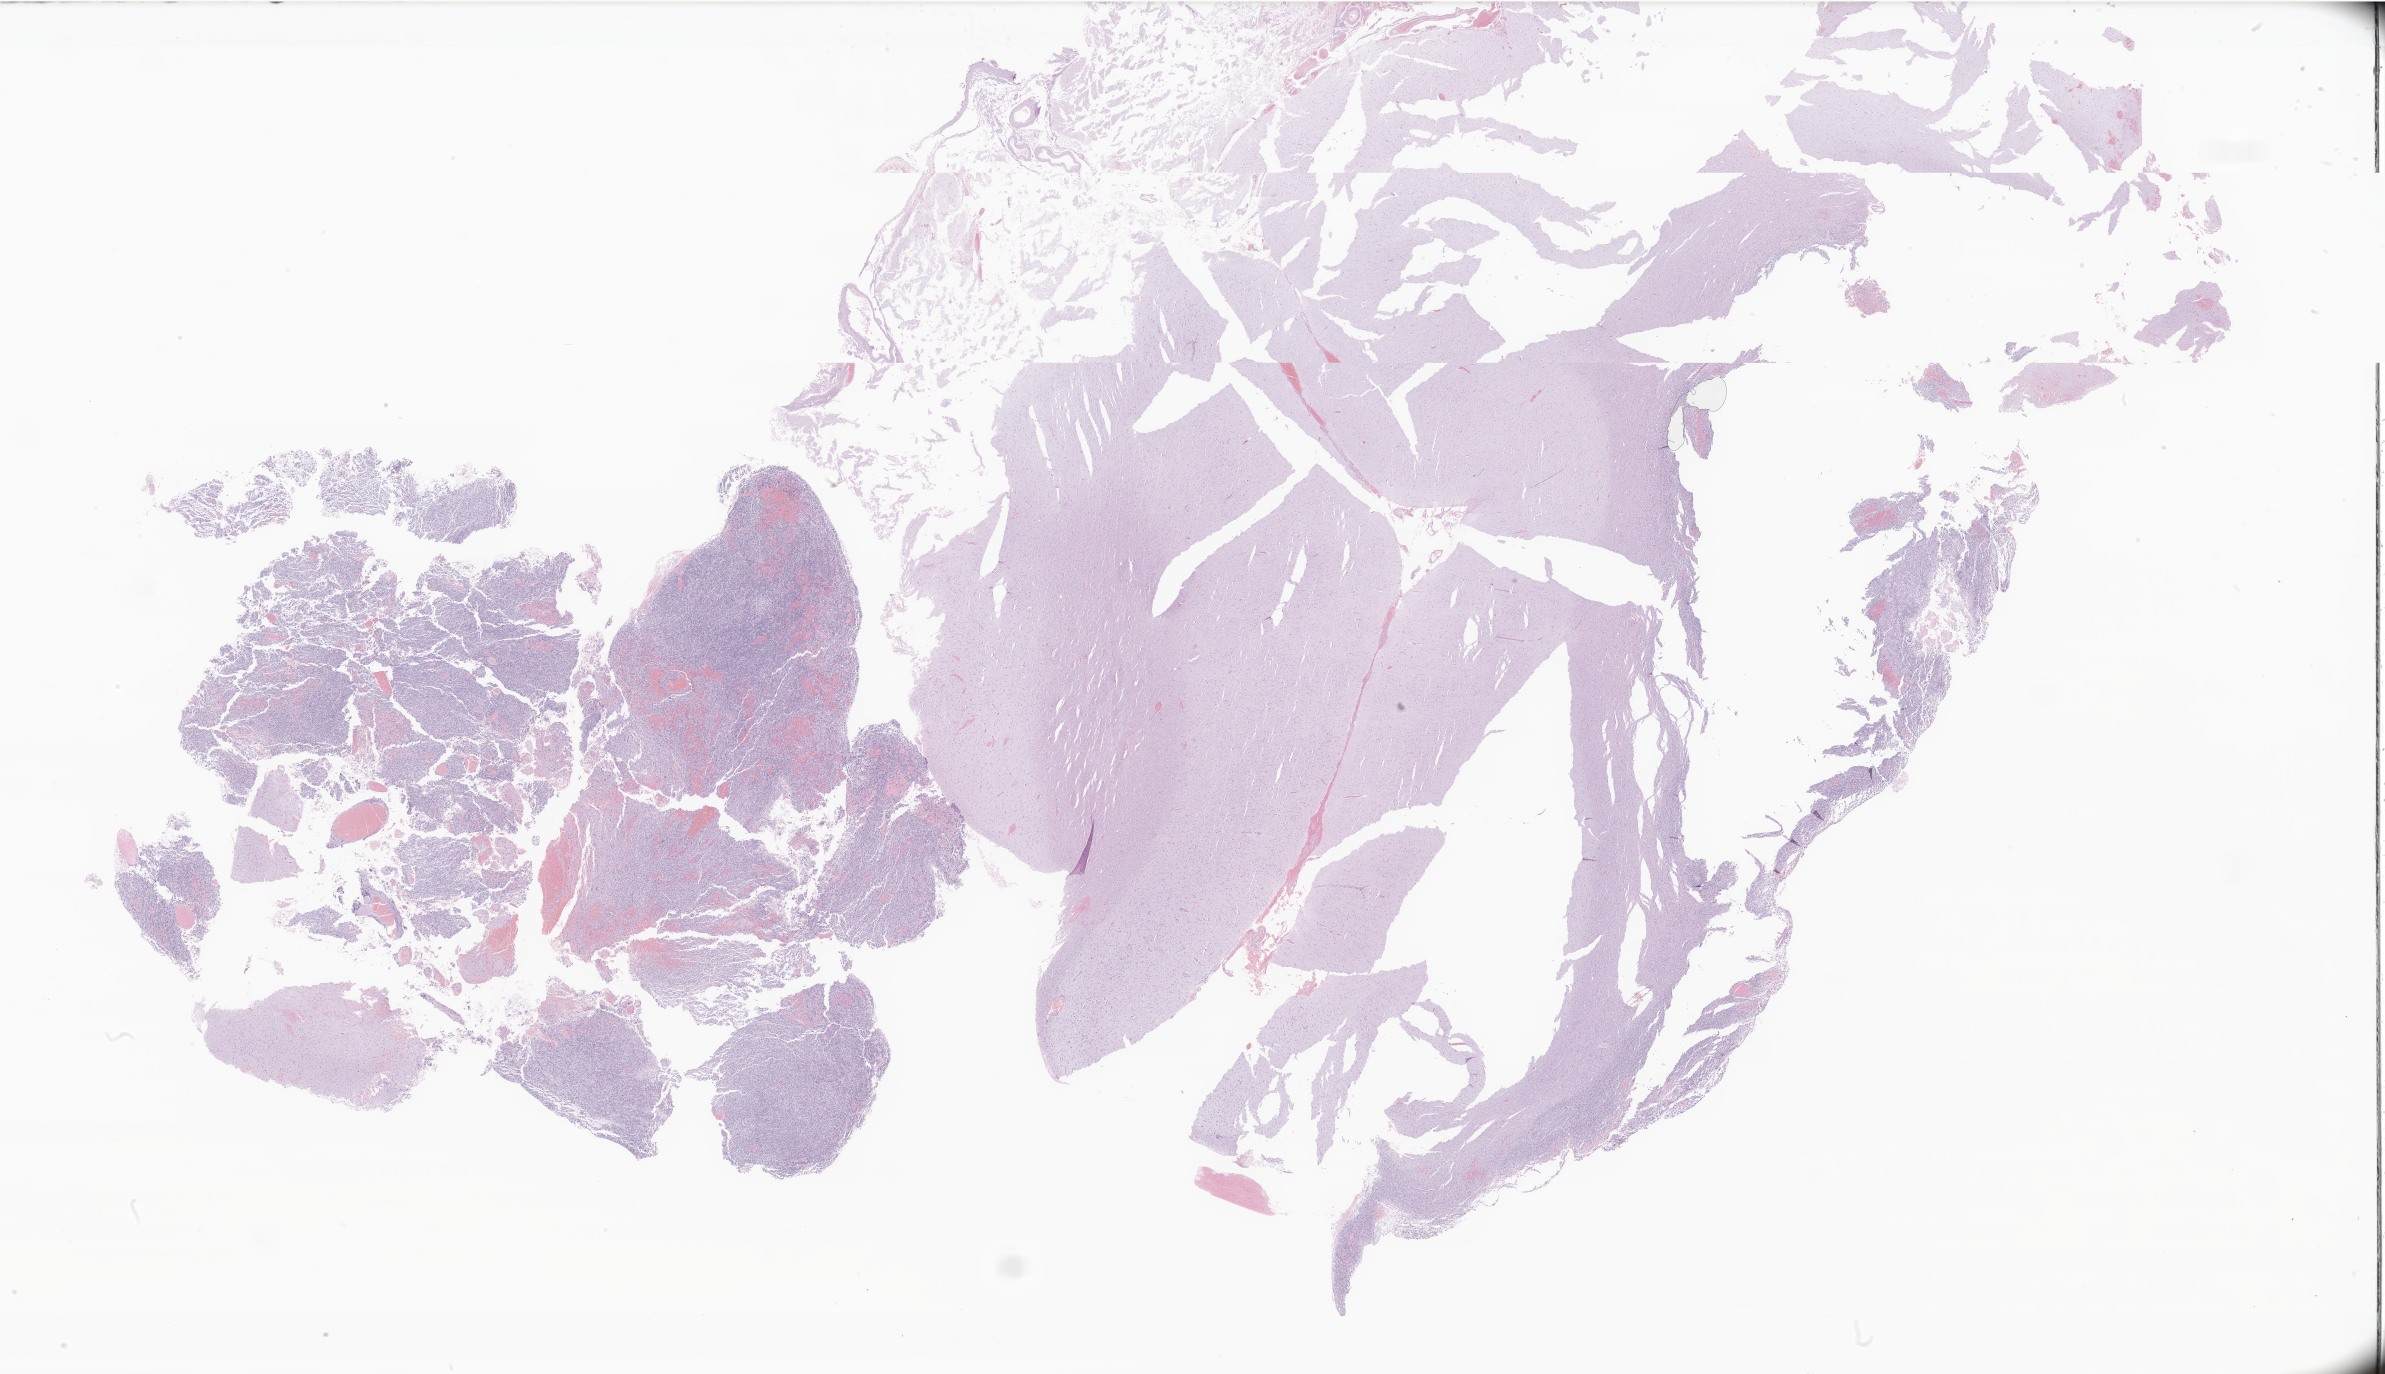
Digitized H&E-stained section of tumor tissue from the brain — low-resolution overview of the scanned area, about 40.2 x 23.2 mm, formalin-fixed paraffin-embedded section. Patient: male, age 269 months (22 years 5 months).
Diagnosis (ICD-O-3 morphology term): Glioma, malignant.